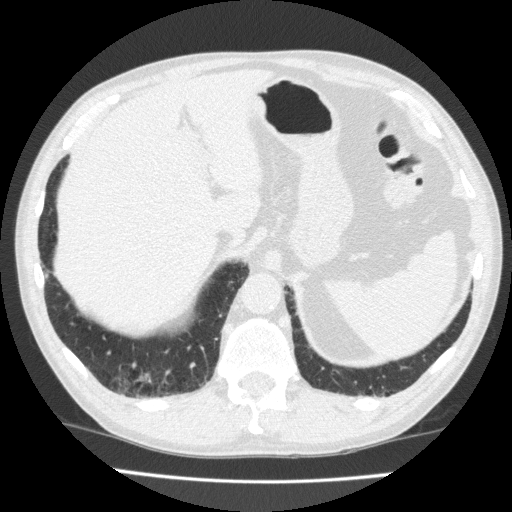
Chest CT (low-dose screening protocol), one axial image, first (baseline) screen, lung window (W 1500 / L -600 HU). Male, age 70 years at enrolment. Current smoker at enrolment.
• Expert reader's lesion annotation, box from (x=114, y=360) to (x=164, y=399) px.
• Screening reader's record for this exam: no non-calcified nodule ≥4 mm recorded.
• Official screen result: negative screen, significant abnormalities not suspicious for lung cancer.
• Lung cancer was diagnosed 503 days after this screen (after the second annual screen): squamous cell carcinoma, NOS, right lower lobe, moderately differentiated (G2), stage IA (AJCC 6th edition), 20 mm at pathology.